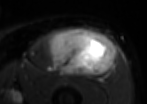
MRI of an extremity soft-tissue mass, one axial slice. Position 47 of 85 along the scan axis. T2-weighted fat-saturated. MR volume resampled by the dataset authors to the PET/CT grid (not the native acquisition matrix). 3.27 mm slice thickness. 147 × 104 image matrix, field of view 144 × 102 mm. Male patient. Case-level facts recorded for this patient, not image findings: histological type: extraskeletal osteosarcoma; grade: high; site of the primary tumour: thigh.
Annotated regions visible in this slice (expert contour drawn on MRI and transferred to this co-registered scan by the dataset authors):
- gross tumour volume (mass): bounding box (x1, y1, x2, y2) in pixels: (49, 28, 114, 75)